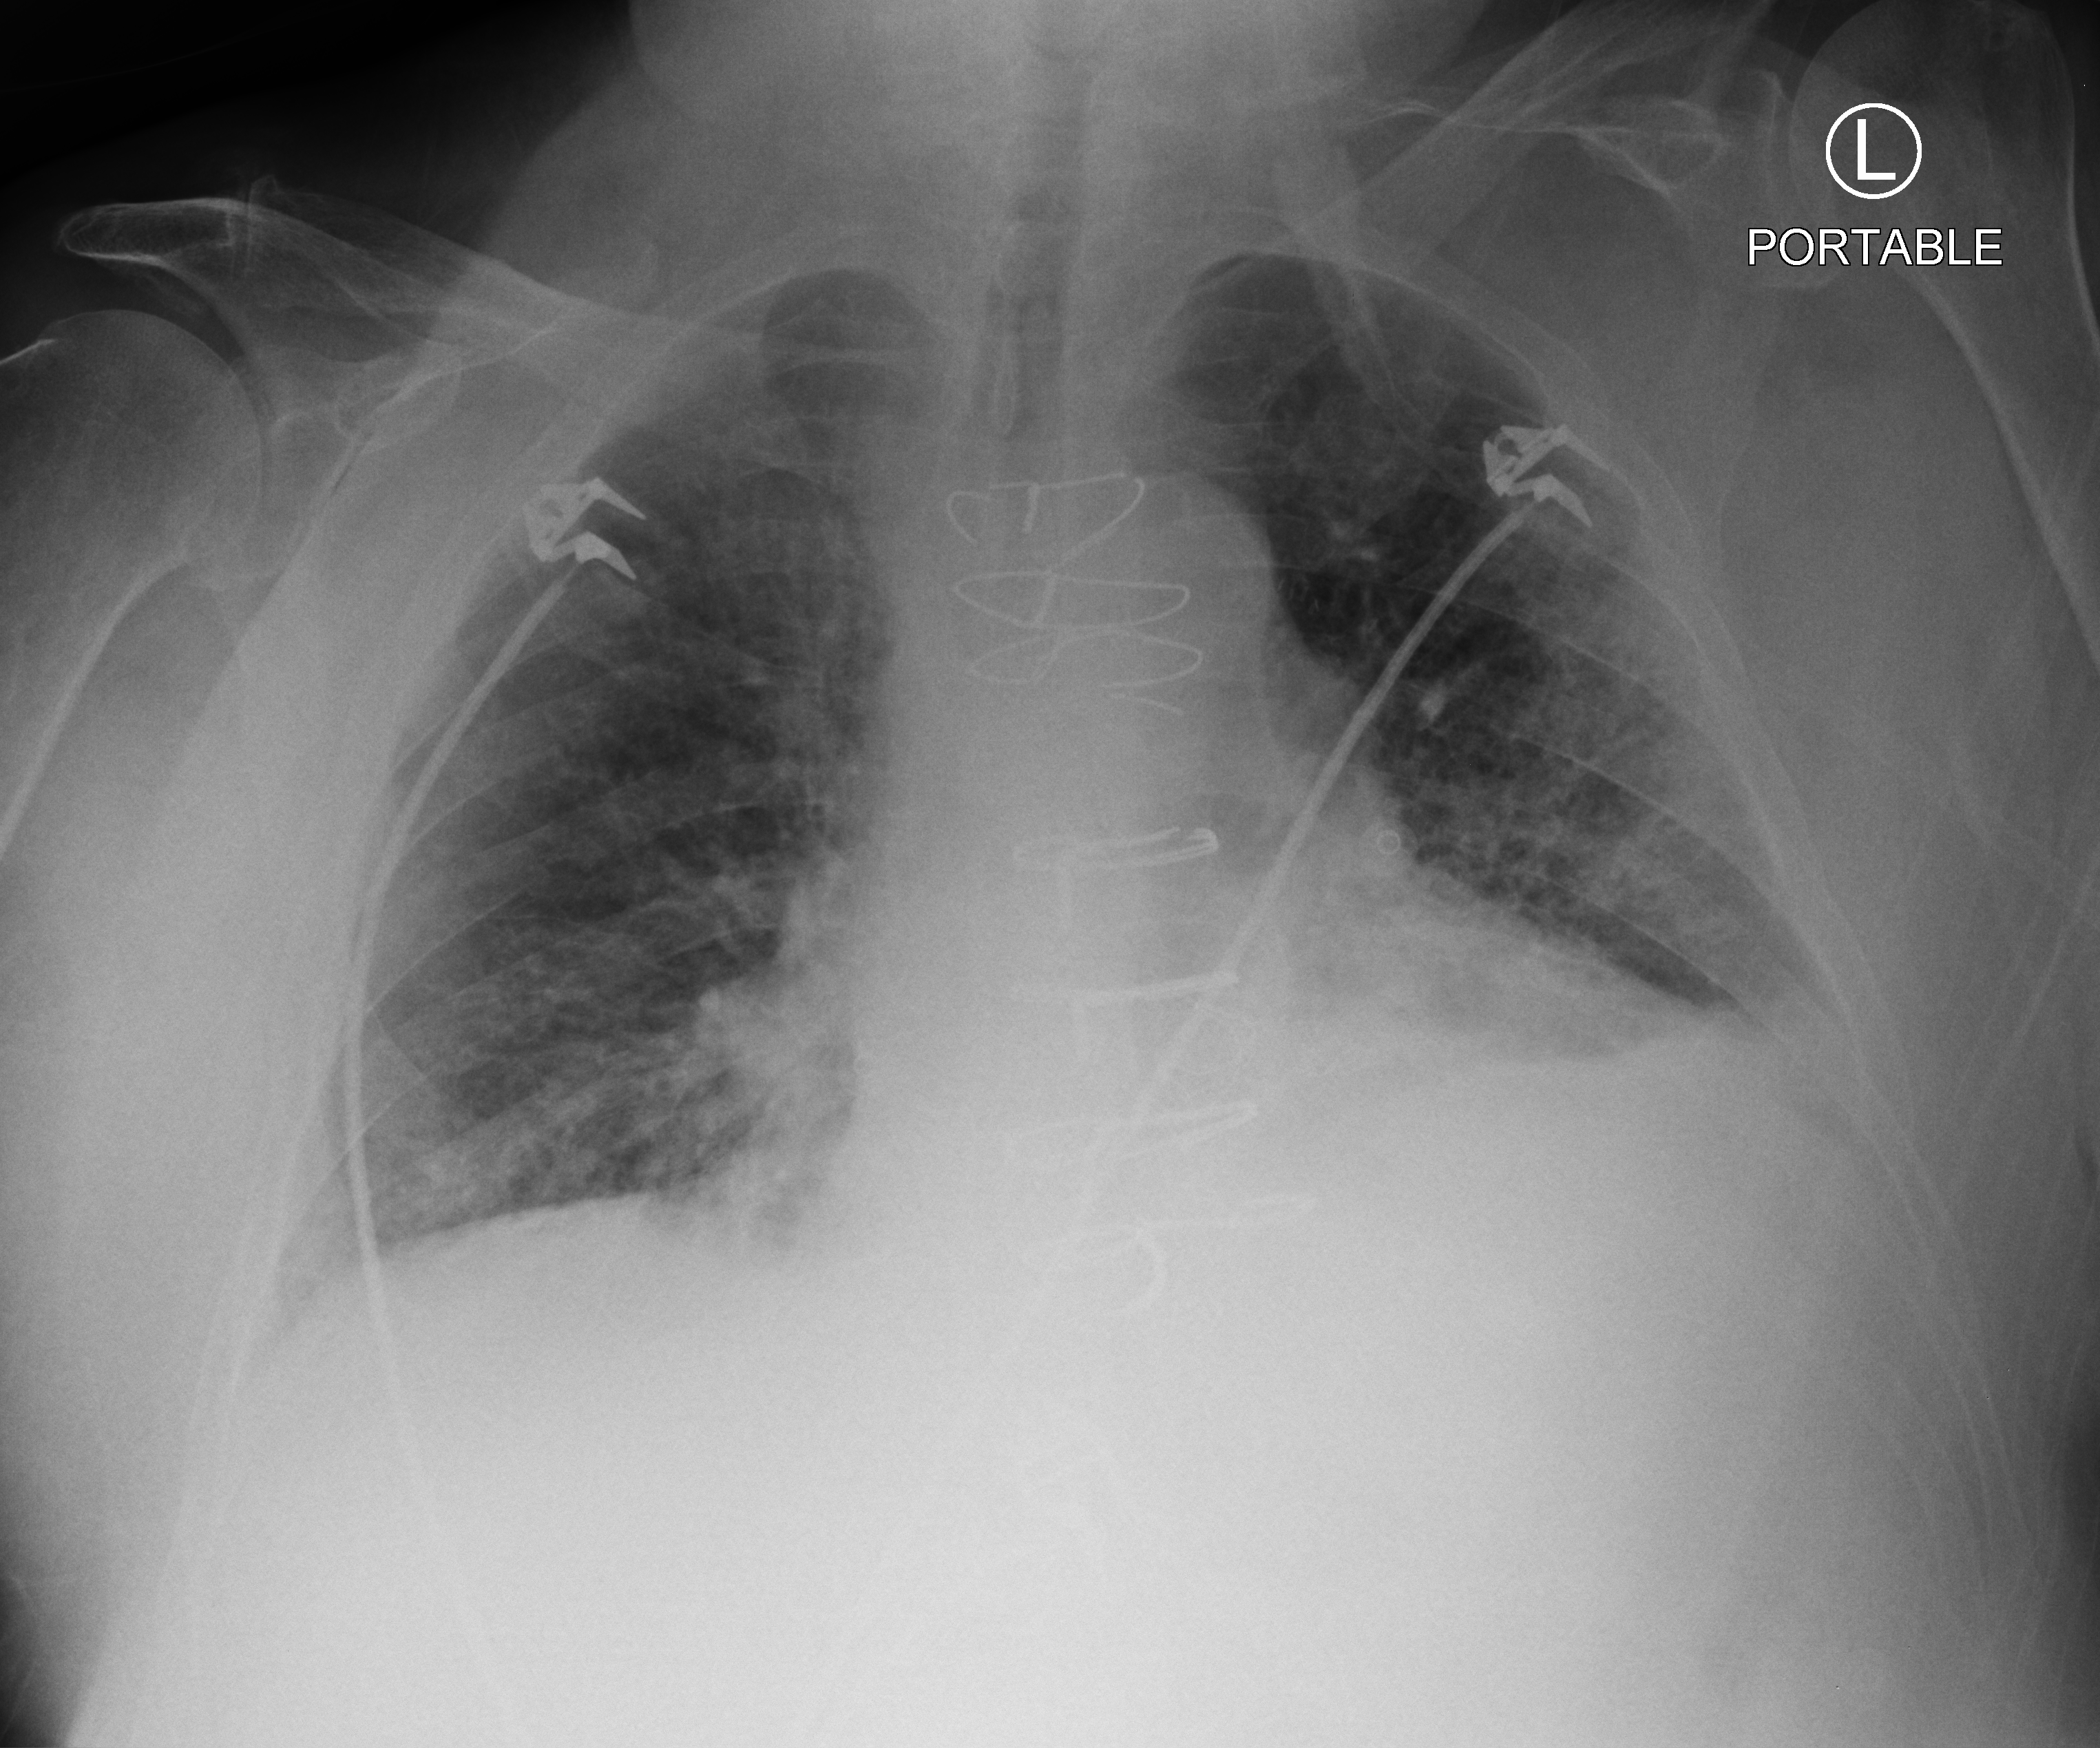
Bedside chest radiograph (computed radiography). Male patient hospitalised with COVID-19, age 75–90 years.
From the hospital-stay record, not from the radiograph (when in the stay this image was taken is not recorded):
- mechanically ventilated during this hospital stay: no
- chronic kidney disease (admission record): yes